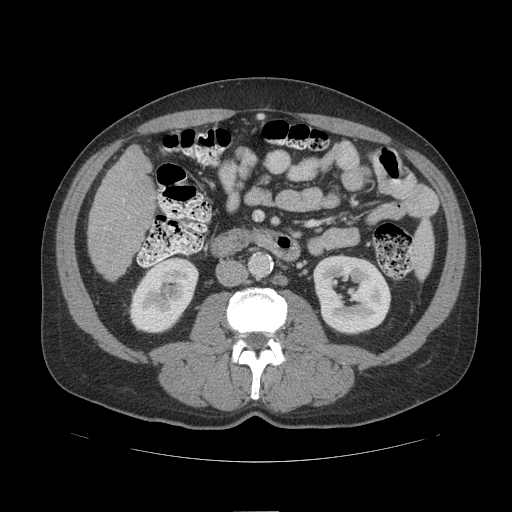
Contrast-enhanced abdominal CT (liver protocol), one axial slice; position 34 of 109 along the scan axis; 140 kVp; soft-tissue window (W 400 / L 40 HU); 2.5 mm slice thickness; 512 × 512 image matrix. From the clinical record (not read from this slice): diagnosis: hepatocellular carcinoma (patient treated with transarterial chemoembolisation; whether this scan precedes or follows treatment is not stated here); TNM stage (as recorded): Stage-IIIB; Child-Pugh class: A; tumour differentiation: poorly differentiated.
Outlined on this slice (semi-automatic segmentation, software-assisted and operator-edited):
- liver parenchyma outside the tumour (the mass and vessels are separate outlines, so this box may not span the whole liver): bounding box <88,146,154,280> (left, top, right, bottom; pixels)